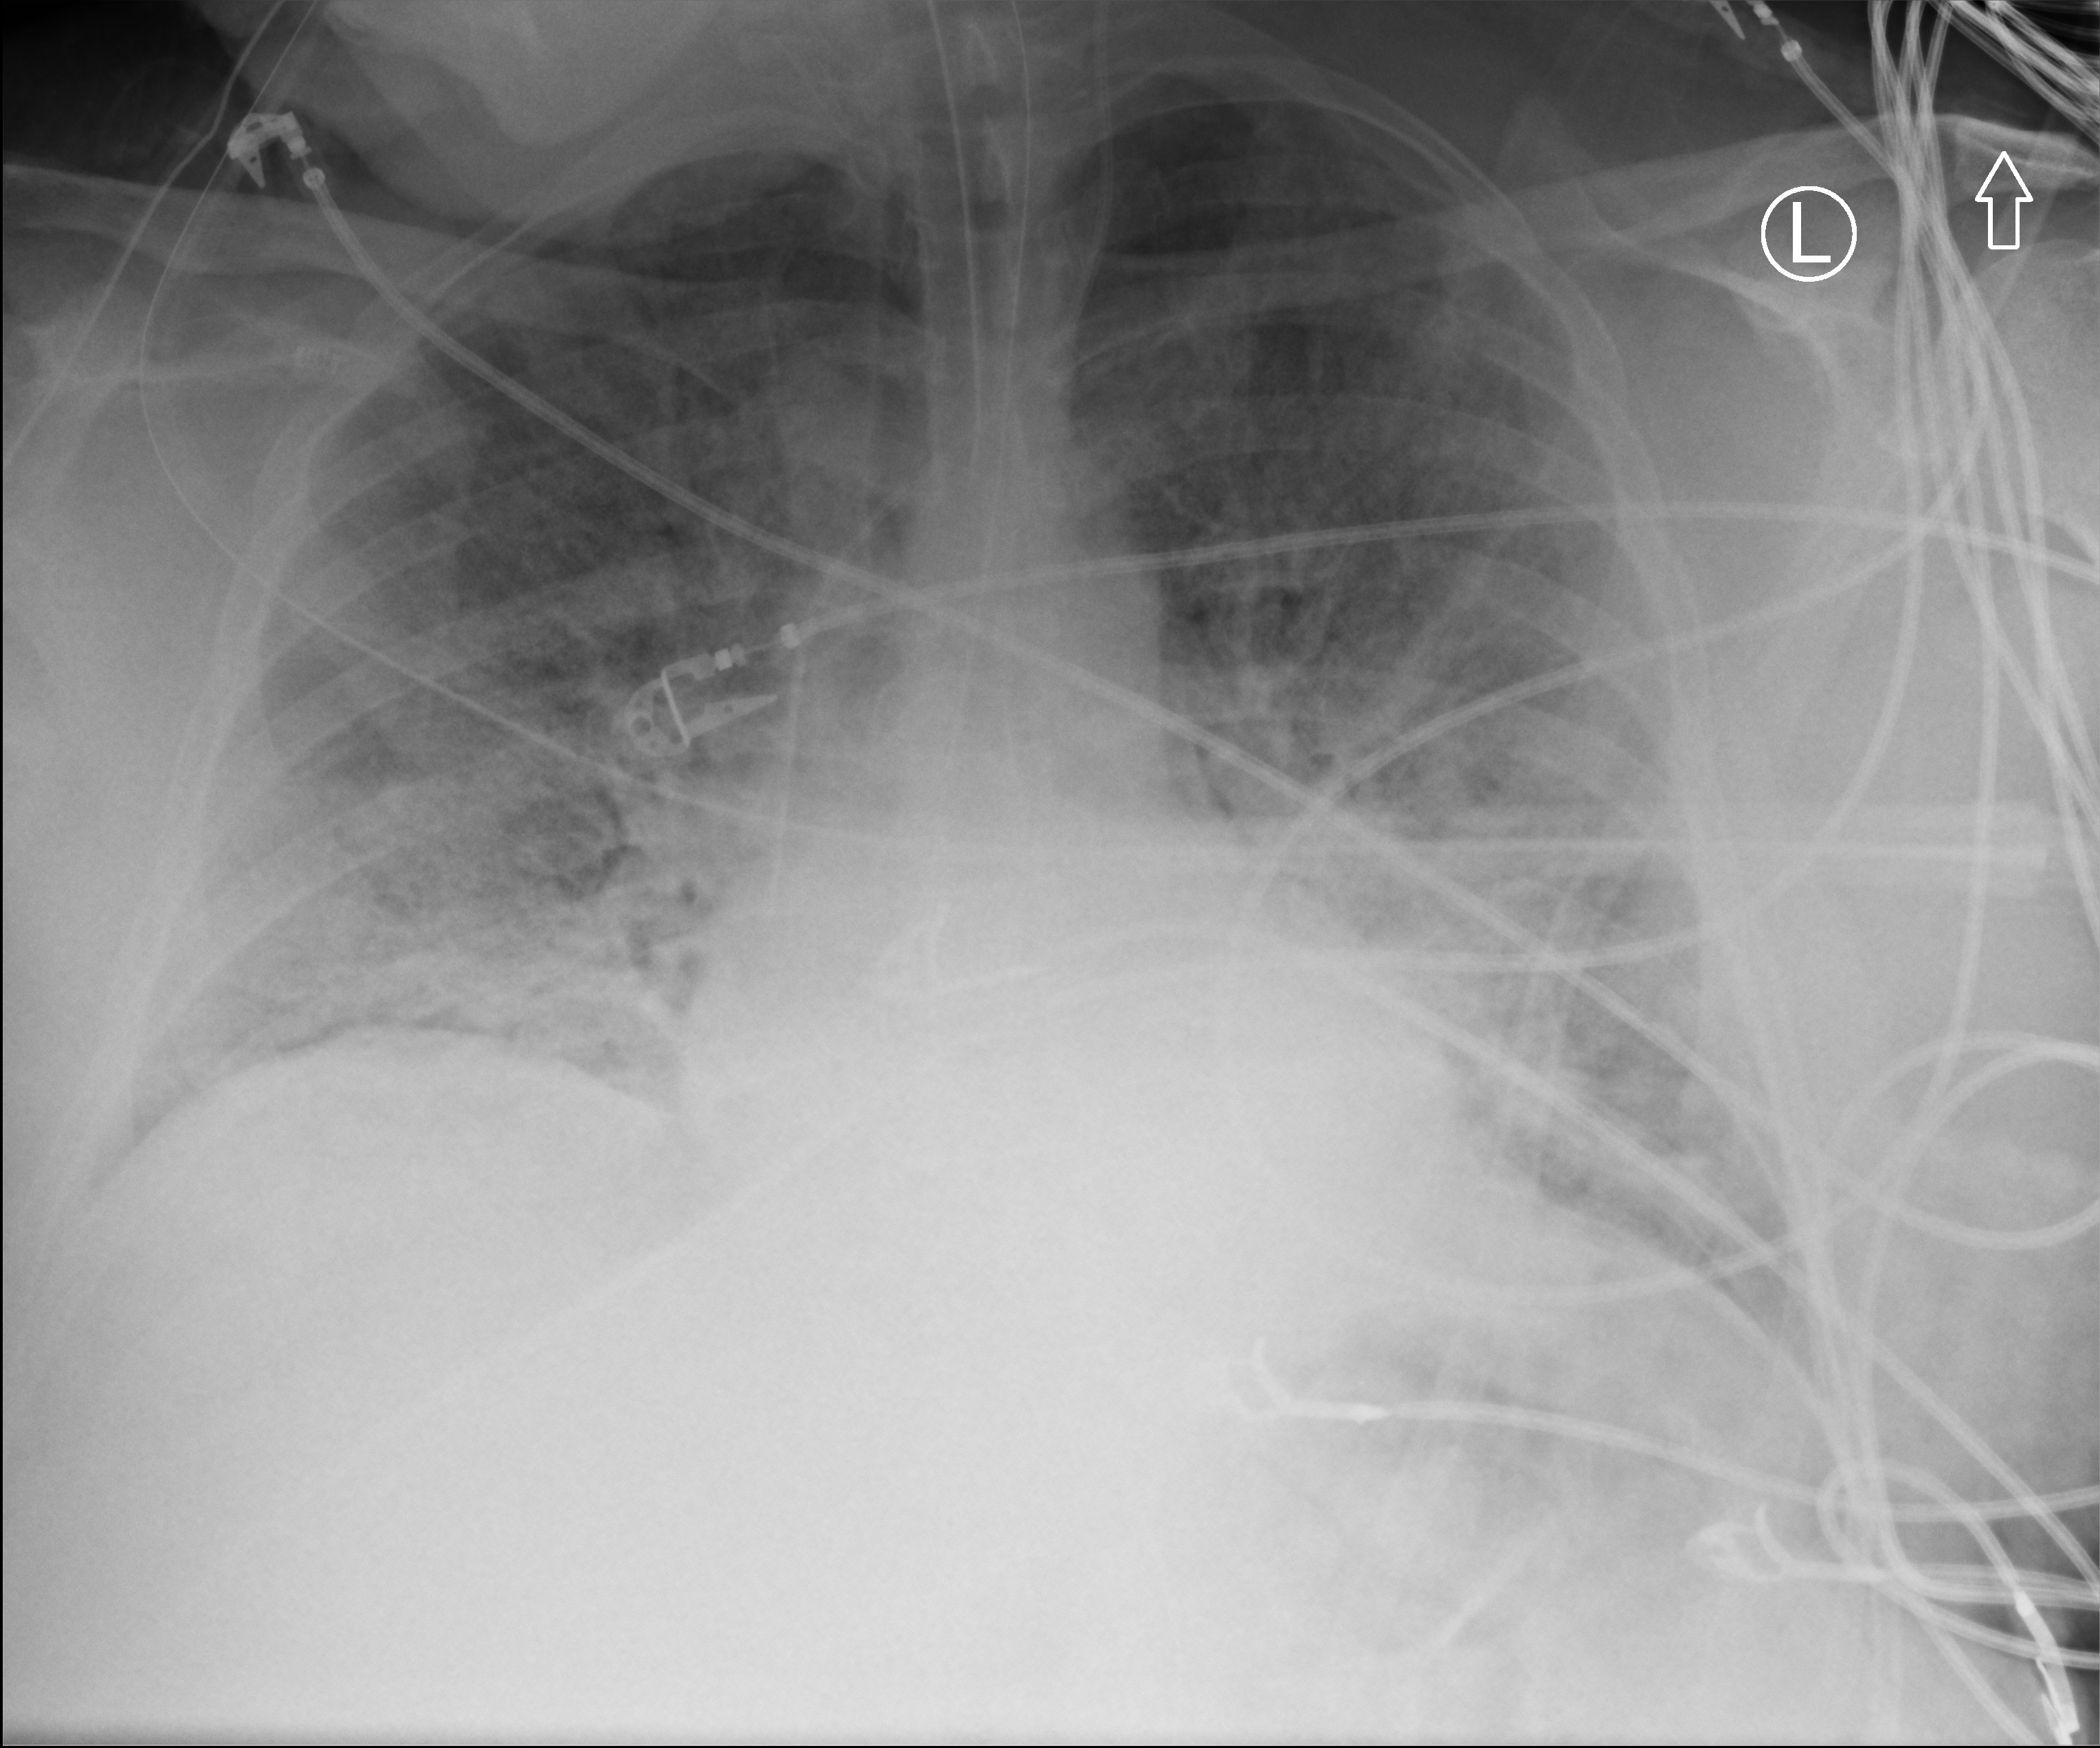
Portable chest radiograph, anteroposterior (AP) projection. Patient hospitalised with COVID-19, aged 18–59 years.
Admission-level facts for this patient (not findings on this image; timing relative to this image not recorded): mechanically ventilated during this hospital stay: yes; length of hospital stay: 16 days; admitted to intensive care during this hospital stay: yes.